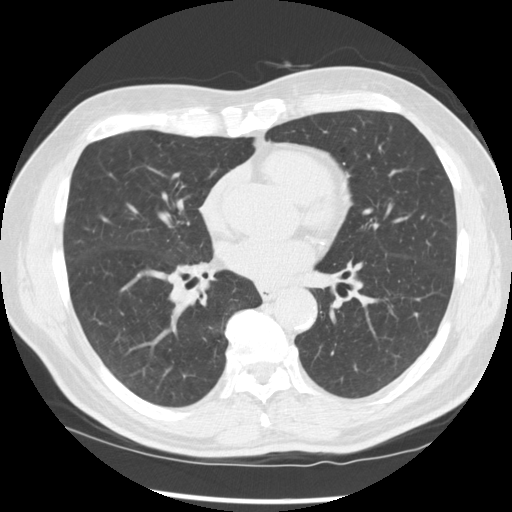
Low-dose screening chest CT, one axial slice; slice 133 of 277 in the series (ordered by position); reconstruction kernel STANDARD; lung window (W 1500 / L -600 HU); 2.5 mm slice thickness; 512 × 512 image matrix.
Annotated regions visible in this slice (expert manual segmentation):
- lesion 1 (tumor, middle lobe of right lung): bounding box [x1, y1, x2, y2] px = [170, 287, 201, 306]